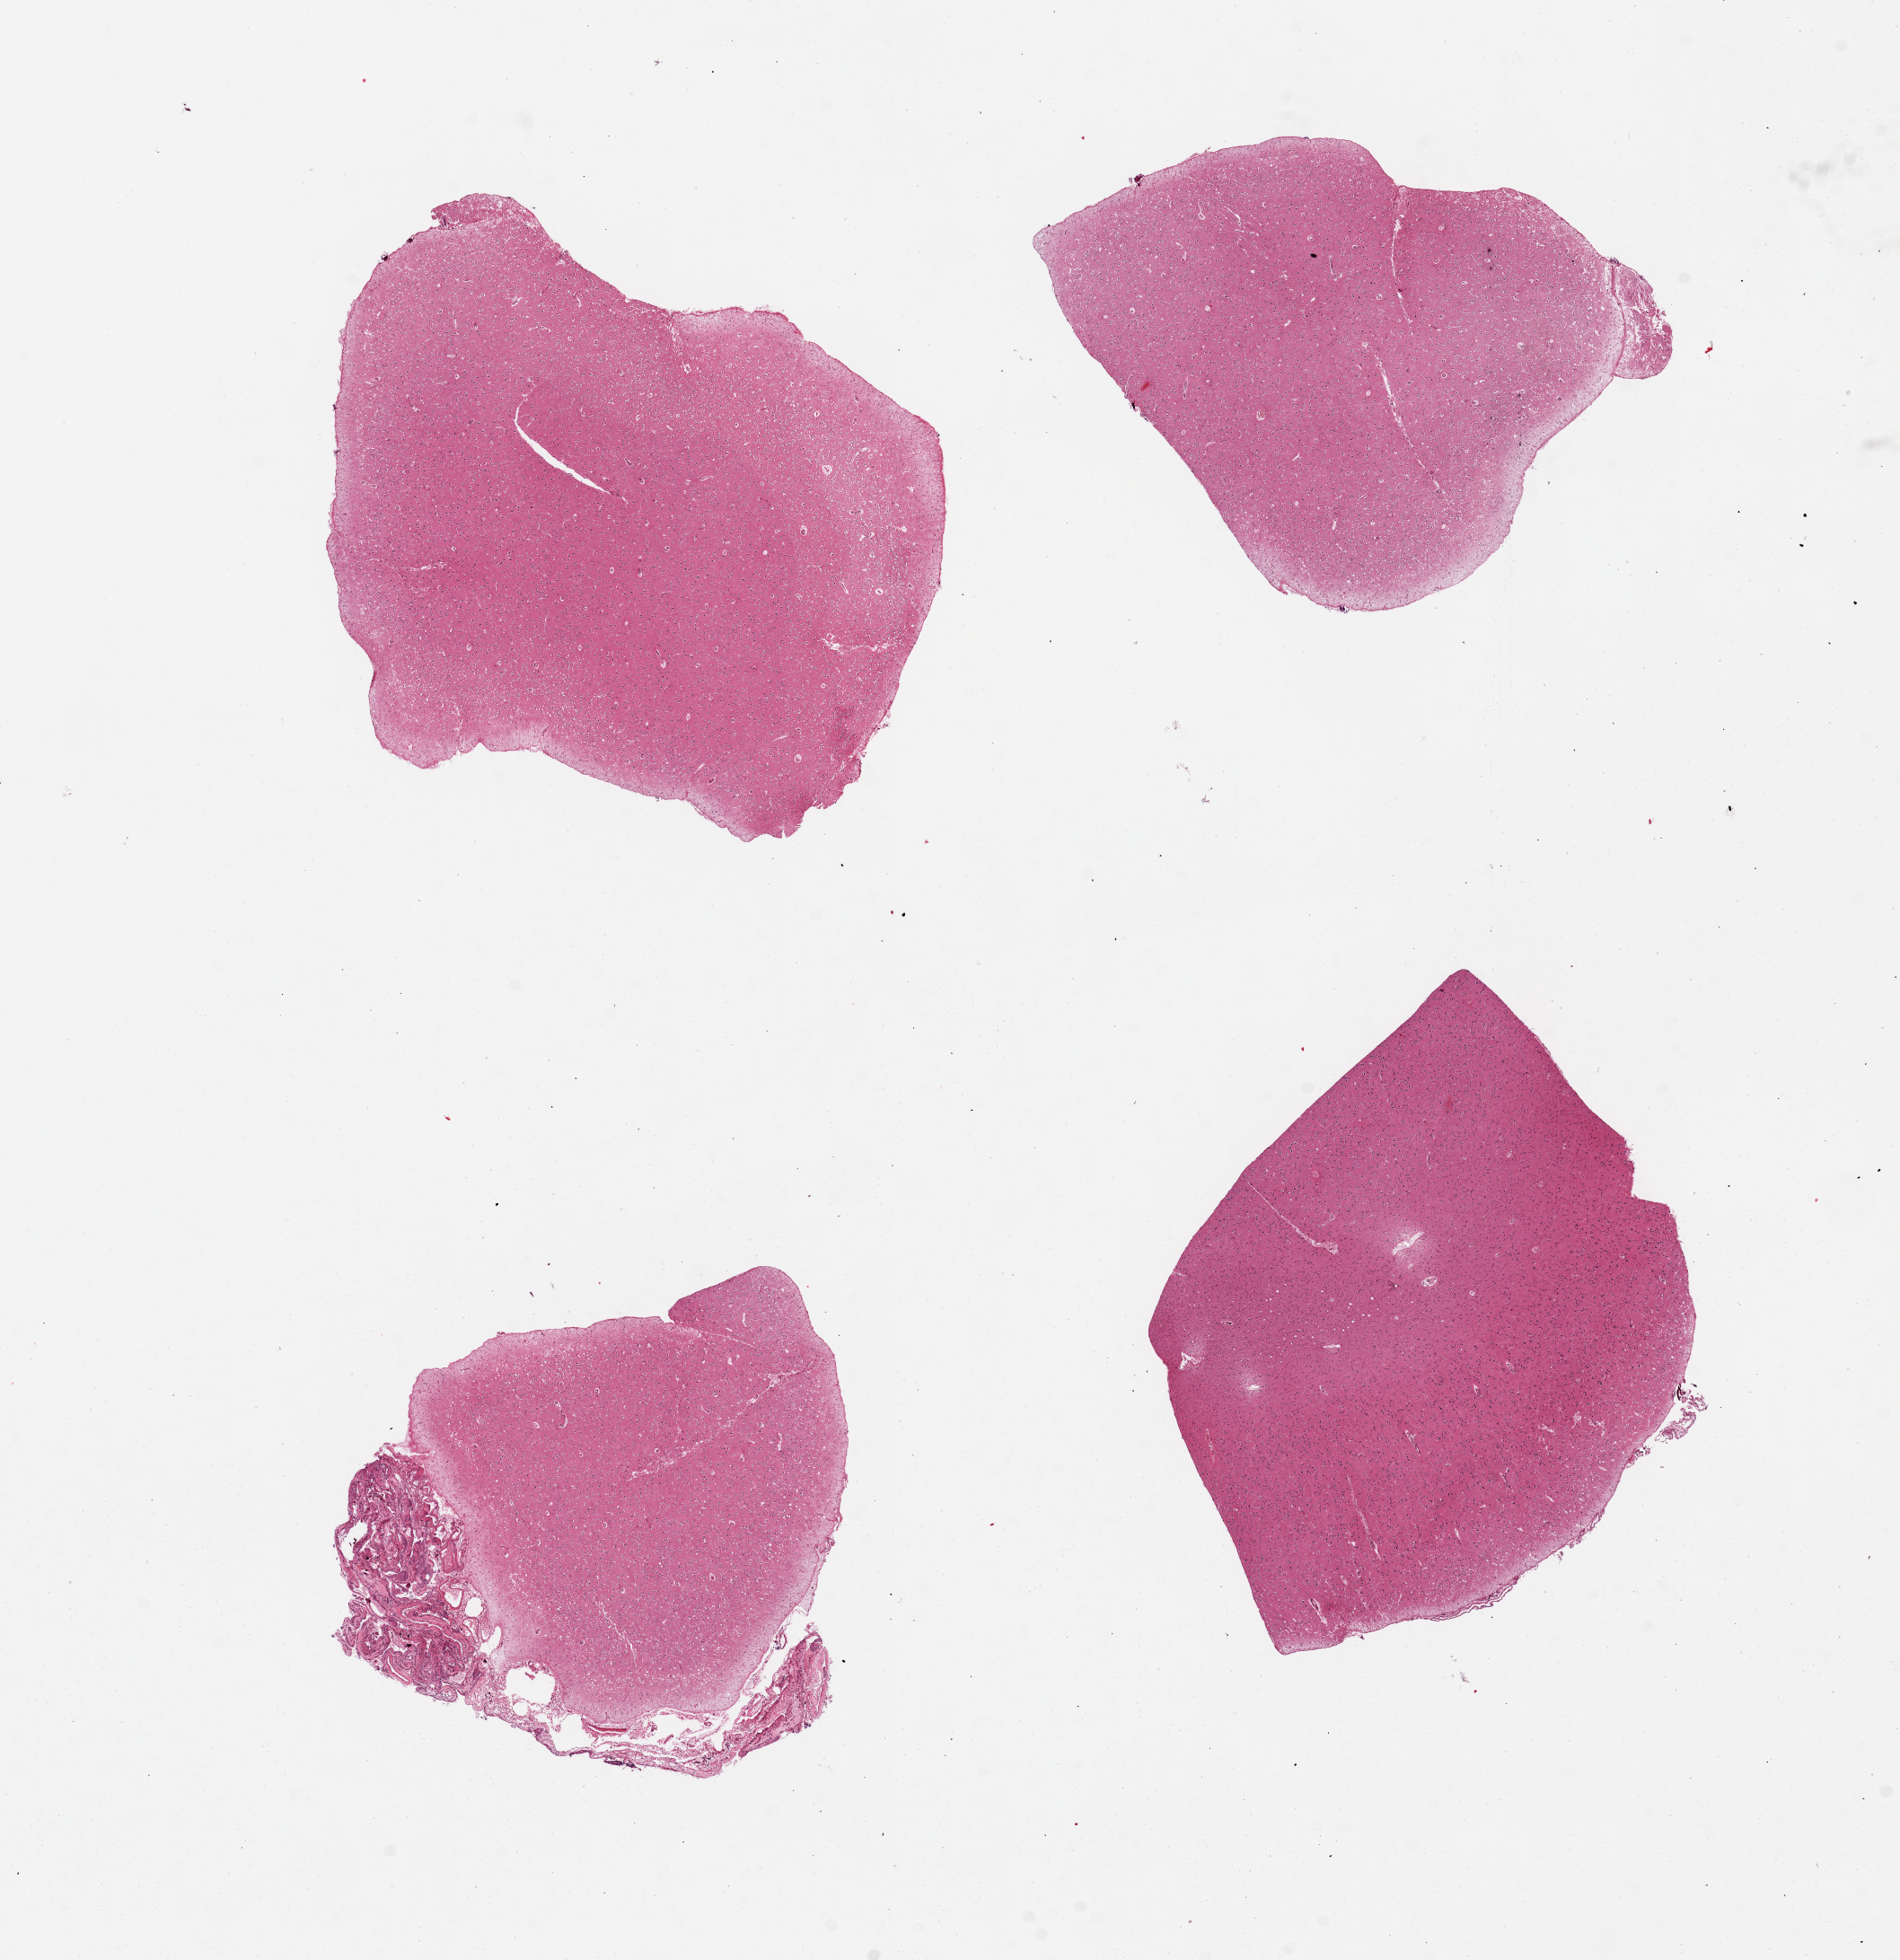
Digitized hematoxylin and eosin (H&E)-stained section, whole scanned area (about 16.7 x 17.3 mm, from a 20x scan) shown as a low-resolution overview. PAXgene-fixed paraffin-embedded (PFPE) section. Target tissue: cerebral cortex. Donor tissue sample. Donor sex: female.
Pathologist's review note for this sample: 4 pieces, ahdherent meninges/vessels on one section.